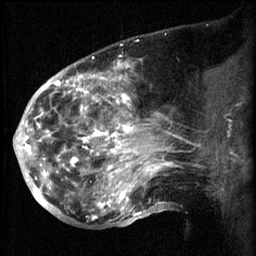
Breast MRI (dynamic contrast-enhanced), one sagittal slice; slice 27 of 60 in the series (ordered by position); 3 images stored at this slice position (order not interpretable as contrast timing); 1.5 T; TE 4.2 ms, TR 8.2 ms; 2.3 mm slice thickness; 256 × 256 image matrix, field of view 200 × 200 mm. Female patient, age 50 years.
Annotated regions visible in this slice (semi-automatic segmentation, software-assisted and operator-edited):
- analysis volume of interest (the breast-tissue region the enhancement analysis was run in; not a lesion): box from (x=50, y=64) to (x=169, y=217) px
- tumour enhancement mask (voxels above the 70 % enhancement threshold inside the analysis volume of interest): (x=50, y=64)–(x=169, y=217)